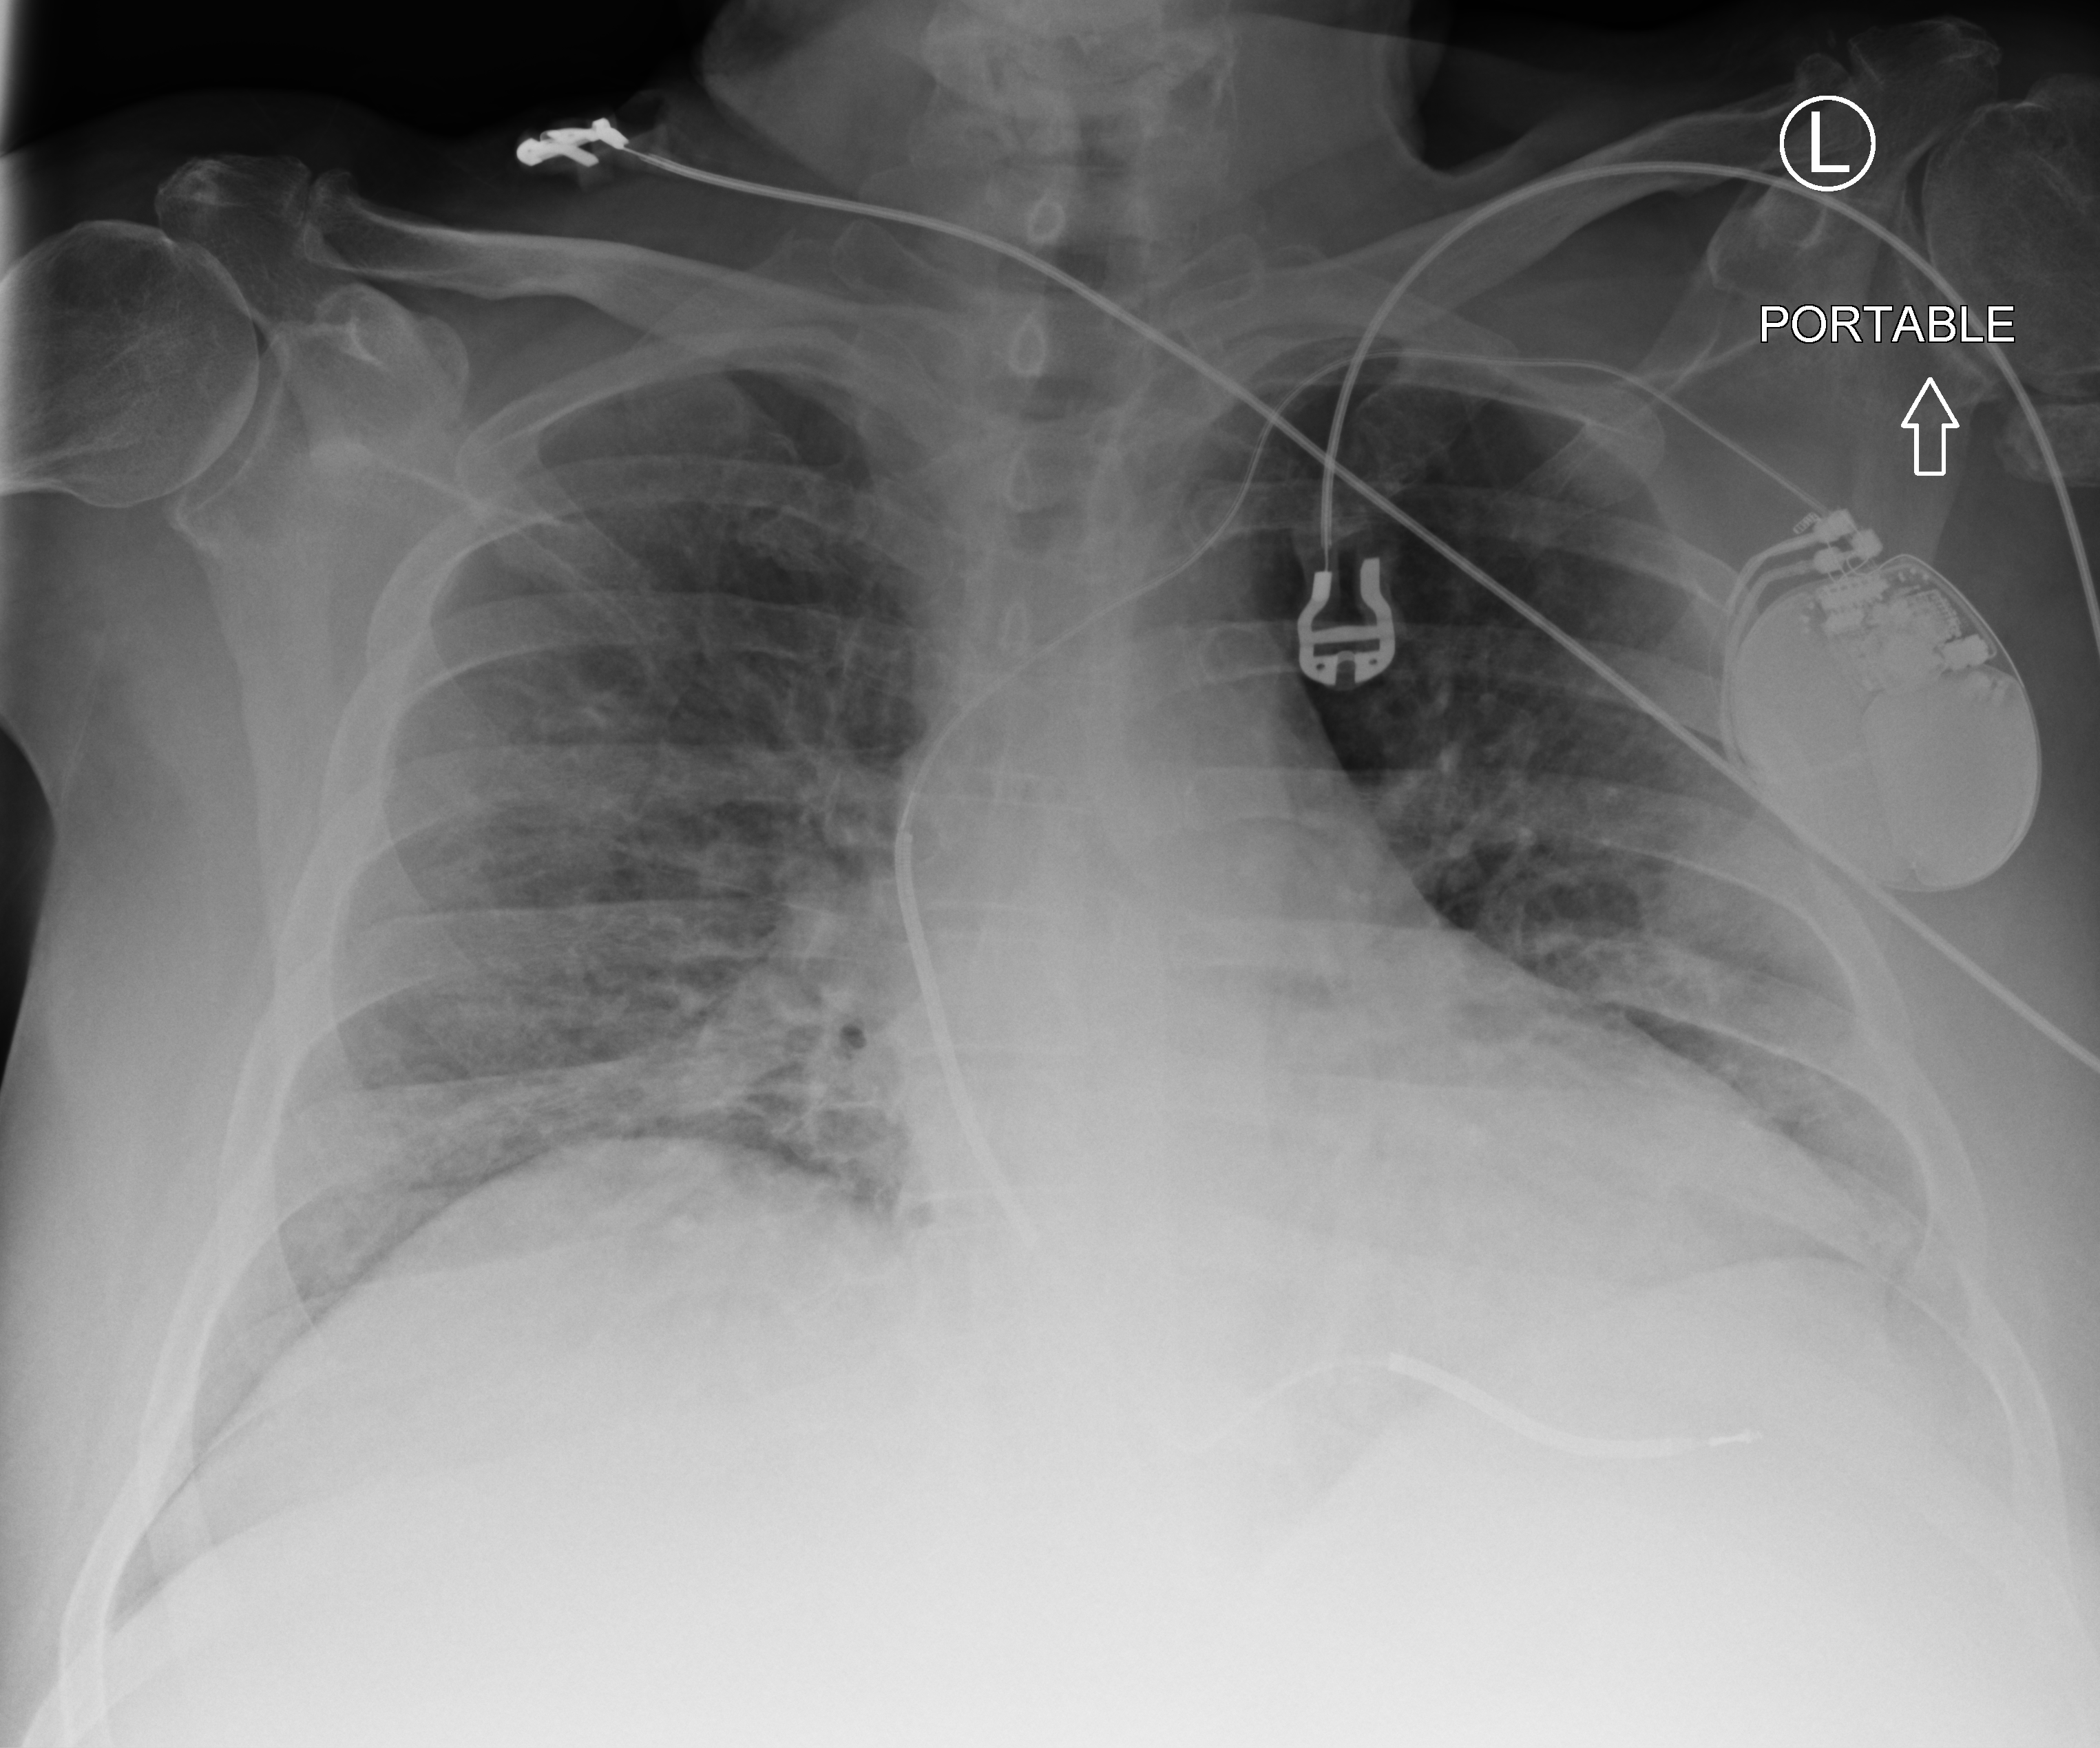
Portable chest radiograph; anteroposterior (AP) projection. Male patient hospitalised with COVID-19, age 60–74 years.
From the hospital-stay record, not from the radiograph (when in the stay this image was taken is not recorded): mechanically ventilated during this hospital stay: no; COPD (admission record): no.